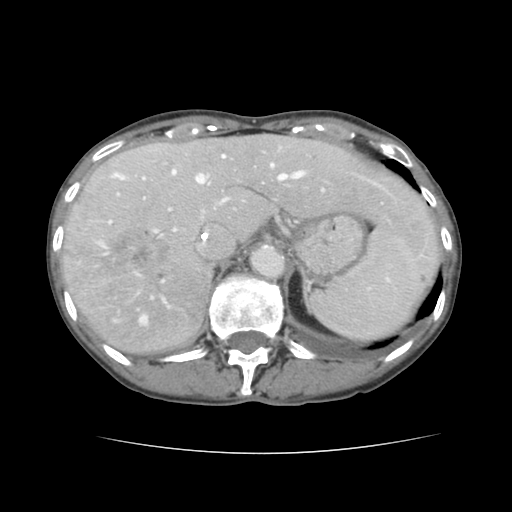
Contrast-enhanced abdominal CT, one axial slice; slice 104 of 136 in the series (ordered by position); 120 kVp; soft-tissue window (W 400 / L 40 HU); 2.5 mm slice thickness; 512 × 512 image matrix, field of view 319 × 319 mm. Female patient, age 77 years. From the clinical record (not read from this slice): diagnosis: colorectal cancer liver metastases, imaged before liver resection; multiple liver metastases: yes; largest metastasis: 3 cm; disease in both lobes: no.
Annotated regions visible in this slice (manually delineated by an expert):
- hepatic veins: bounding box <97,155,389,324> (left, top, right, bottom; pixels)
- liver: <64,136,438,356>
- planned liver remnant (the part of the liver to remain after resection): <160,135,438,266>
- portal vein (with intrahepatic branches): <109,186,384,301>
- liver metastasis: <95,227,176,284>